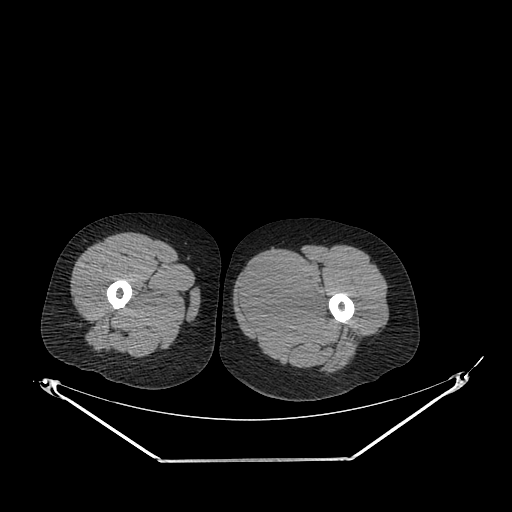
CT of an extremity soft-tissue mass (from a PET/CT study), one axial slice. Slice 235 of 267 in the series (ordered by position). Reconstruction kernel SOFT. Soft-tissue window (W 400 / L 40 HU). 3.75 mm slice thickness. 512 × 512 image matrix, field of view 500 × 500 mm. Female patient. Case-level facts recorded for this patient, not image findings: histological type: pleiomorphic leiomyosarcoma; grade: intermediate; site of the primary tumour: left thigh.
Outlined on this slice (expert contour drawn on MRI and transferred to this co-registered scan by the dataset authors):
- gross tumour volume including surrounding oedema: box from (x=237, y=262) to (x=332, y=334) px
- gross tumour volume (mass): (x=237, y=262)–(x=328, y=330)